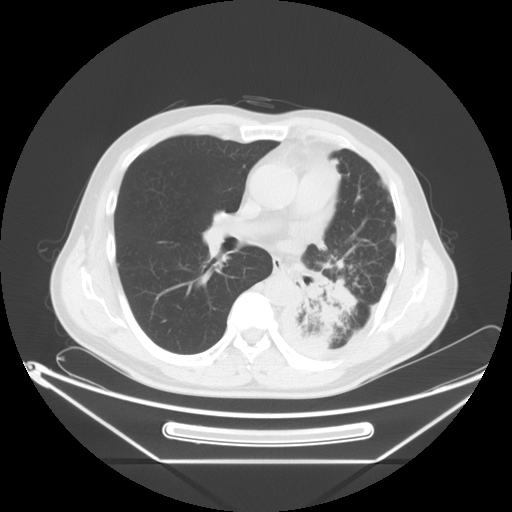
Chest CT, one axial slice. Position 34 of 63 along the scan axis. Lung window (W 1500 / L -600 HU). 512 × 512 image matrix, field of view 442 × 442 mm. Patient: male, 60 years. From the clinical record (not read from this slice): clinical TNM (as recorded): T4 N1 M1.
Structures marked on this image (bounding box drawn by a radiologist):
- lung tumour (recorded histology: adenocarcinoma): bounding box (x1, y1, x2, y2) in pixels: (291, 264, 363, 345)